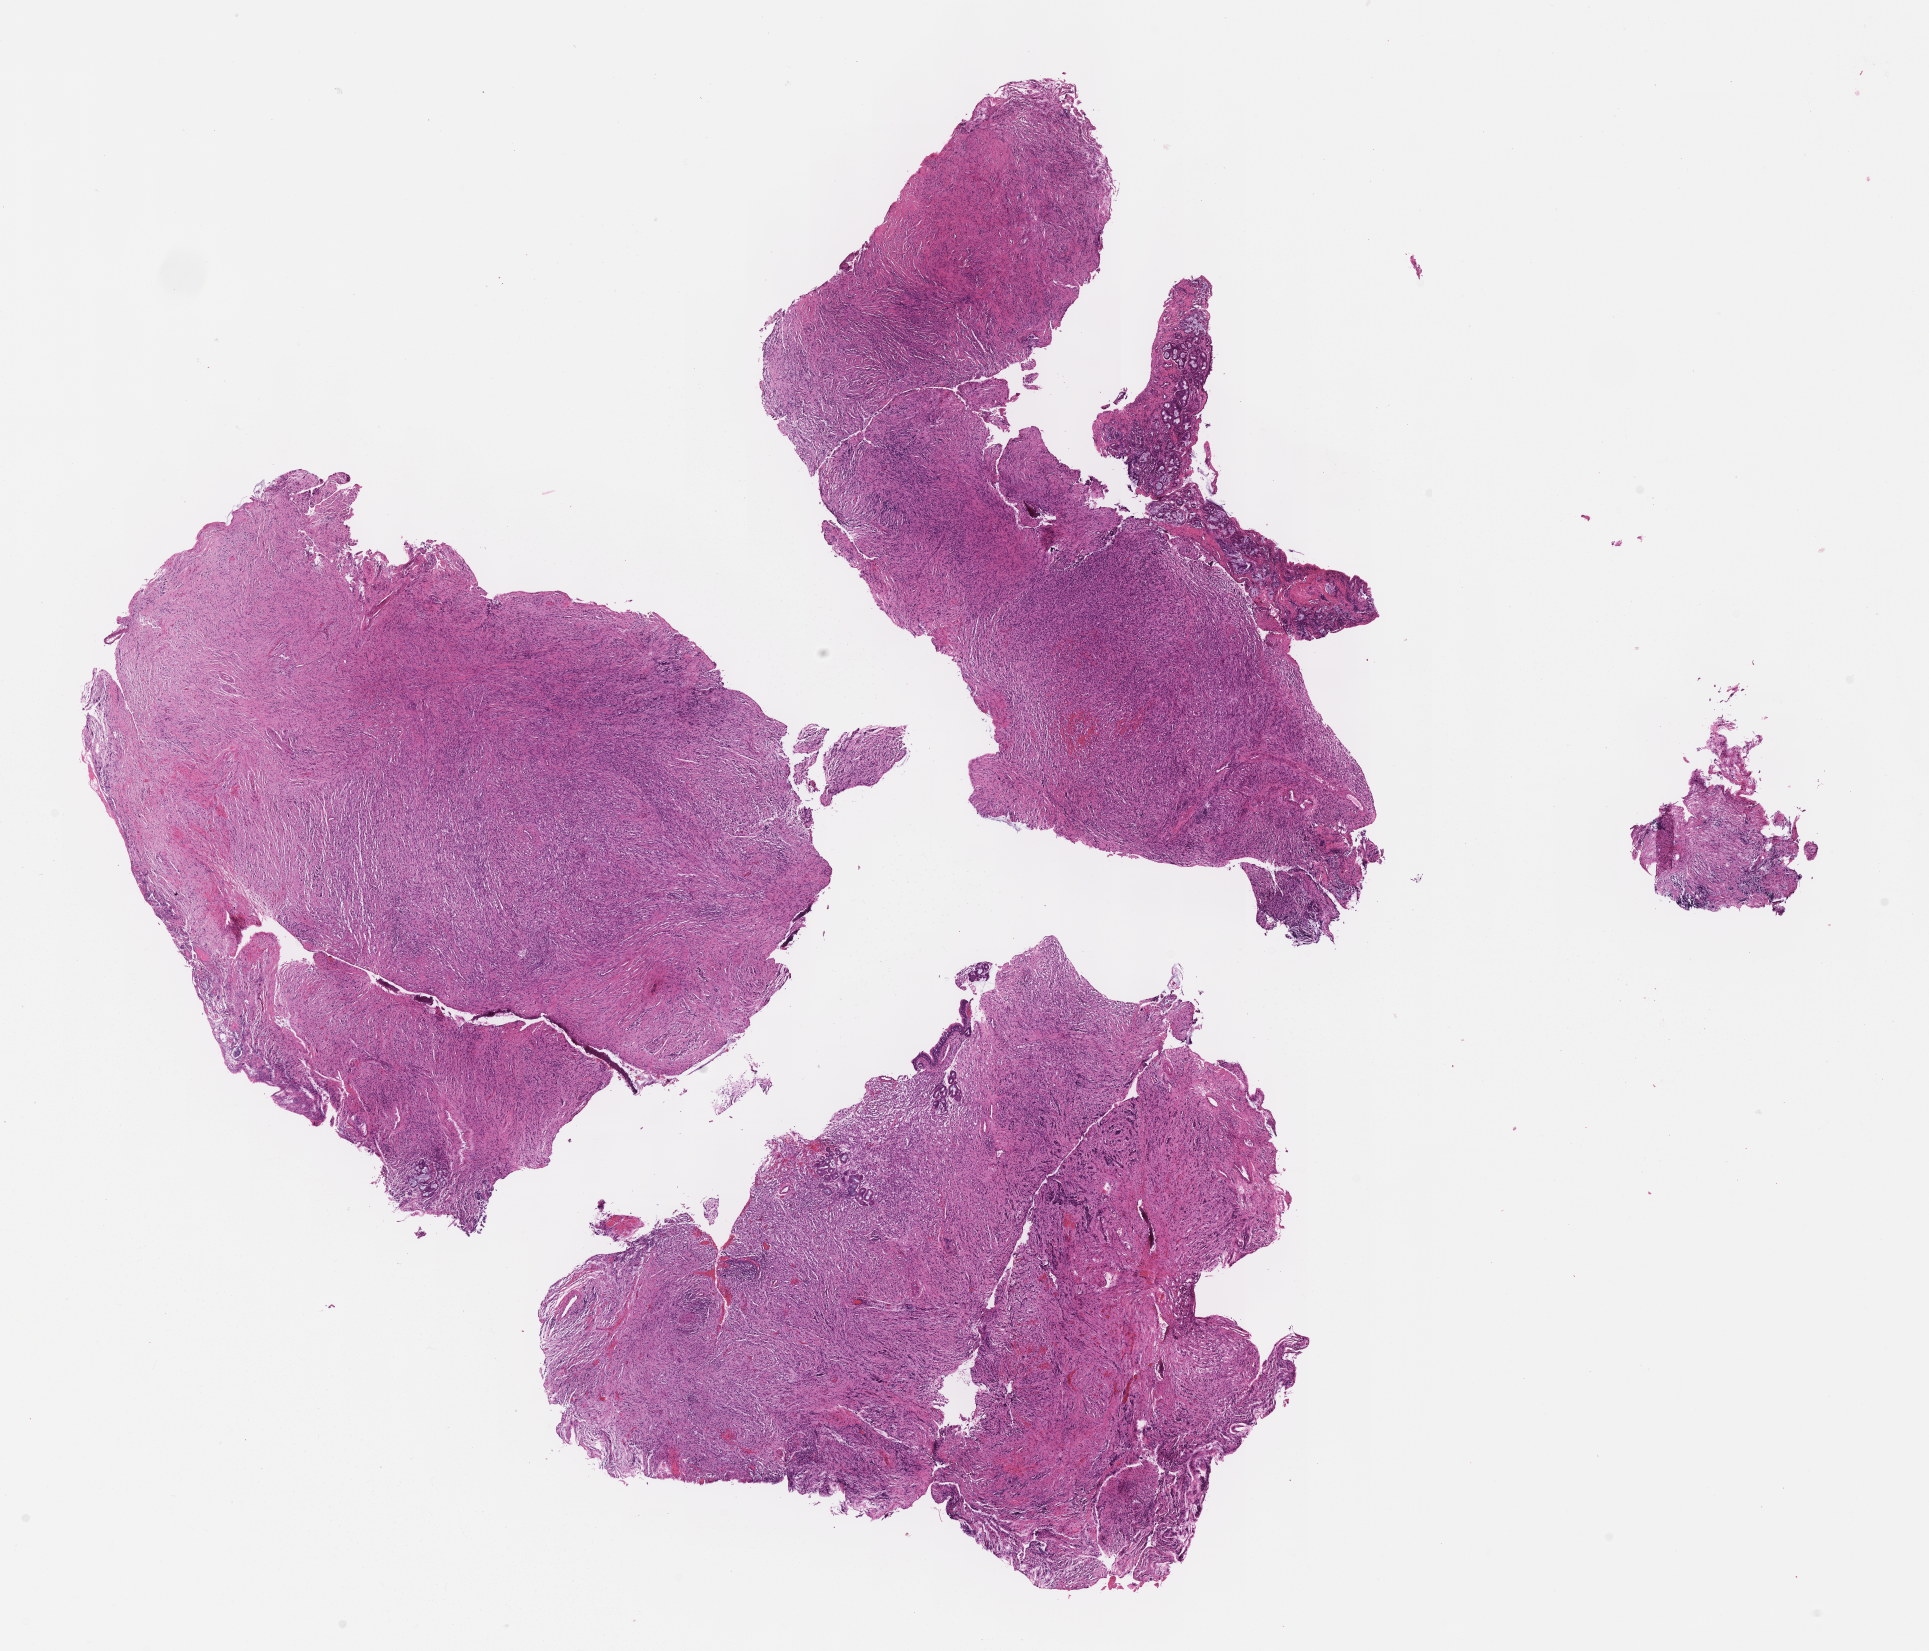
Whole-slide image, hematoxylin and eosin (H&E) stain of tumor tissue — a low-resolution overview of the entire scanned area, about 15.6 x 13.4 mm, formalin-fixed paraffin-embedded section, sample anatomic site: nasal. Female patient, age at diagnosis 2.4 years.
* diagnosis: rhabdomyosarcoma; histological classification: spindle cell rhabdomyosarcoma
* stage (as recorded): 4
* metastatic status at presentation (as recorded): metastatic (confirmed)